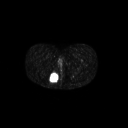
FDG PET of an extremity soft-tissue mass (from a PET/CT study), one axial slice; position 25 of 267 along the scan axis; 128 × 128 image matrix. Female patient, age 17 years. From the clinical record (not read from this slice): histological type: epithelioid sarcoma; grade: intermediate; site of the primary tumour: right buttock.
Annotated regions visible in this slice (expert contour drawn on MRI and transferred to this co-registered scan by the dataset authors):
- gross tumour volume including surrounding oedema: bounding box [x1, y1, x2, y2] px = [48, 72, 59, 83]
- gross tumour volume (mass): [49, 72, 59, 83]